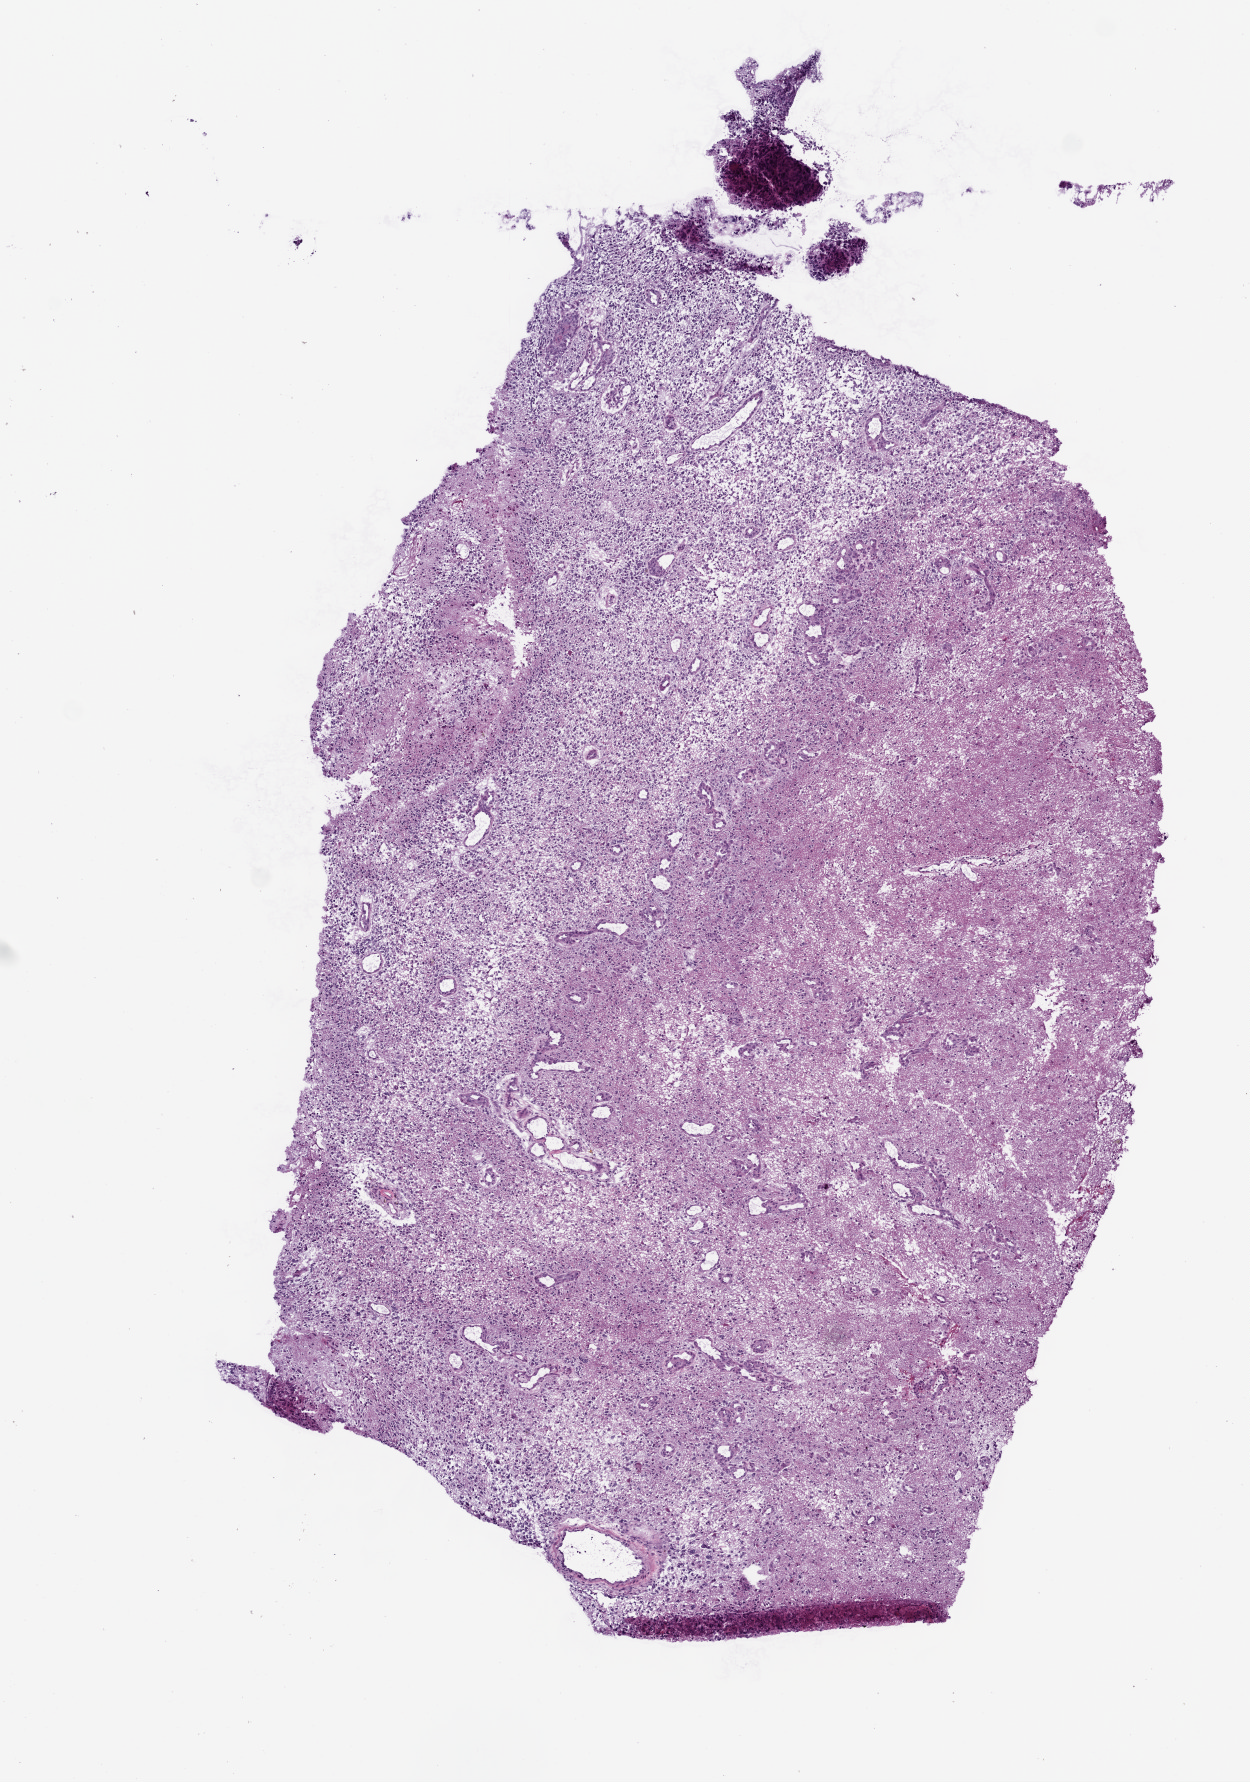
Whole-slide histology image, H&E-stained — low-resolution overview of the scanned area, about 5.0 x 7.1 mm (acquisition: 20x scan); frozen section; sample: primary tumour, brain. Patient: female, age at initial diagnosis 47 years. Slide review estimates, as recorded: tumour cells 98%, tumour nuclei 75%, normal cells 0%, stromal cells 0%, necrosis 2%.
Histologic diagnosis: Glioblastoma.